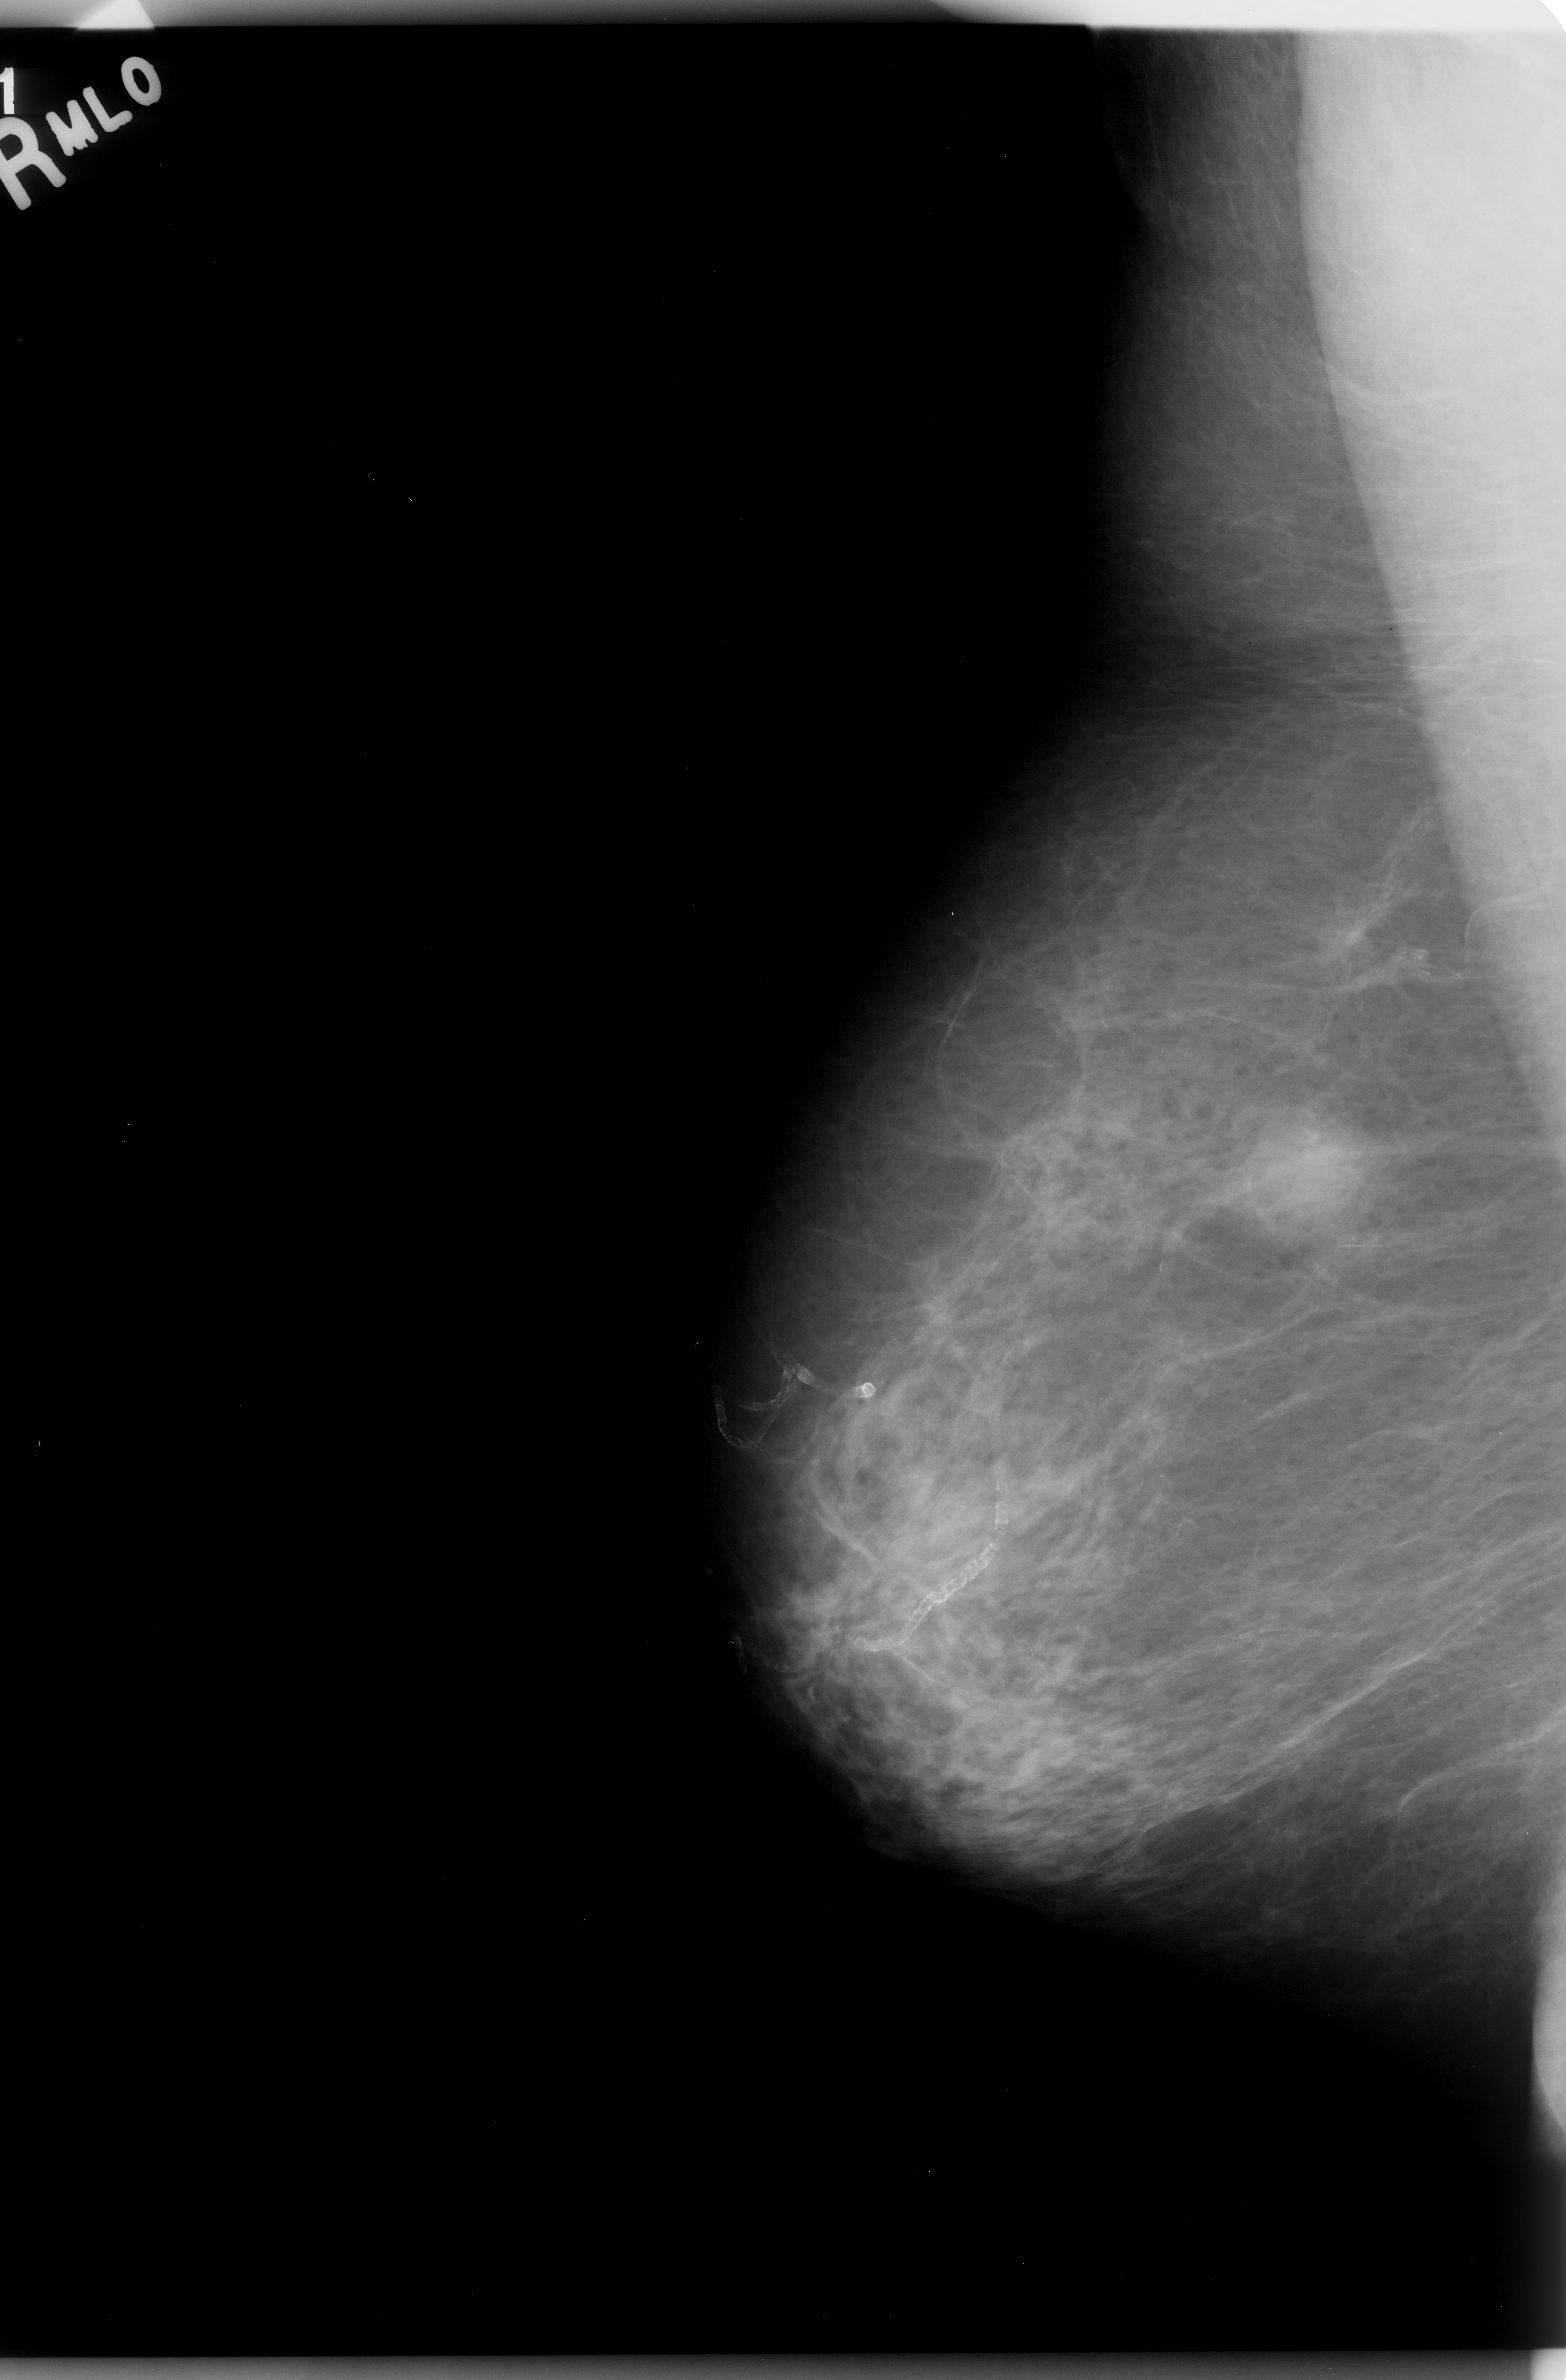
Digitized screen-film mammogram. Right breast. MLO view. Breast composition: almost entirely fatty (BI-RADS density category 1 of 4). 1566 × 2380 image matrix.
Marked abnormalities (boxes around the expert regions of interest):
- mass, shape round, margins ill defined; BI-RADS assessment category 5; pathology result (as recorded, not read from the image): malignant: box from (x=1234, y=1101) to (x=1376, y=1235) px